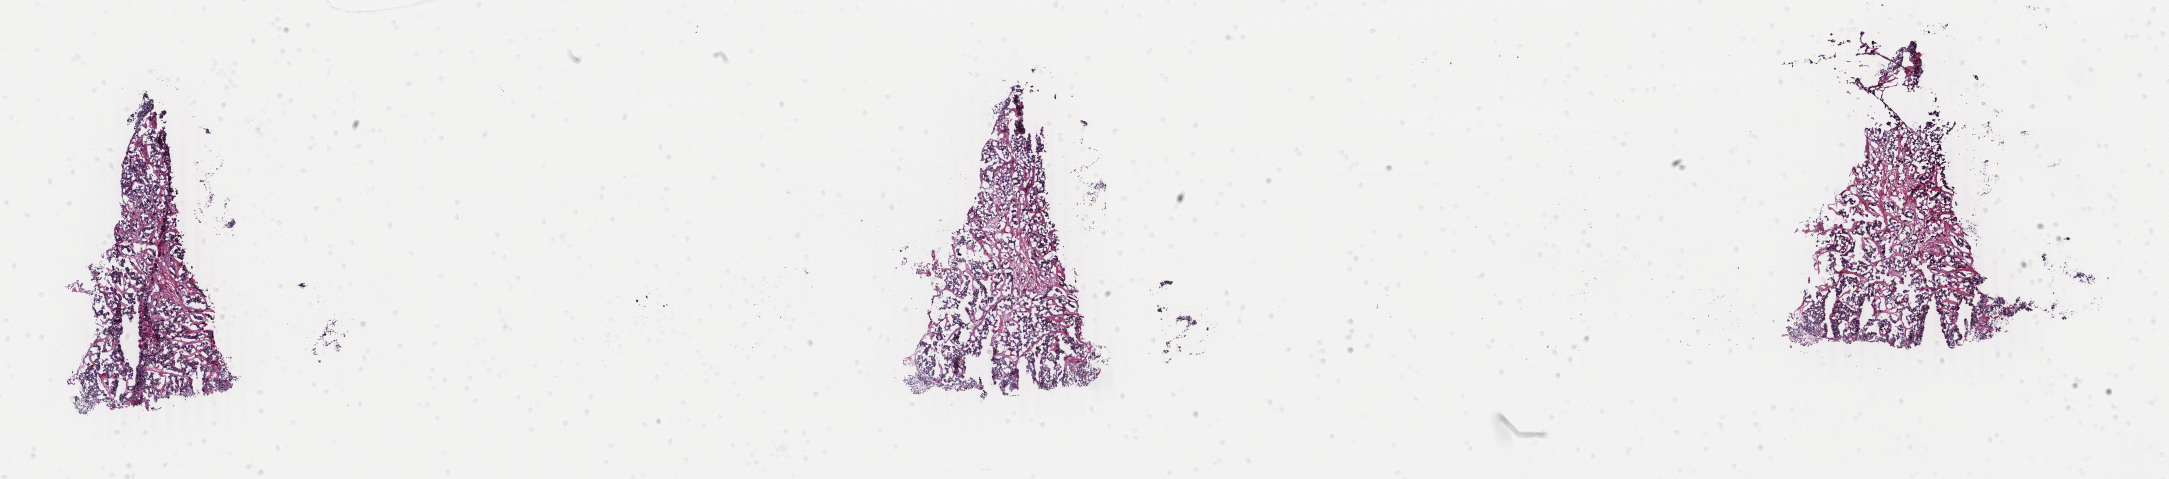
Whole-slide histology image, H&E-stained — whole scanned area (about 34.5 x 7.6 mm, from a 40x scan) shown as a low-resolution overview. Frozen section from the bottom of the tissue portion. Breast, primary tumour sample. Female, age 51 years at initial diagnosis.
Histologic diagnosis: Infiltrating duct mixed with other types of carcinoma.